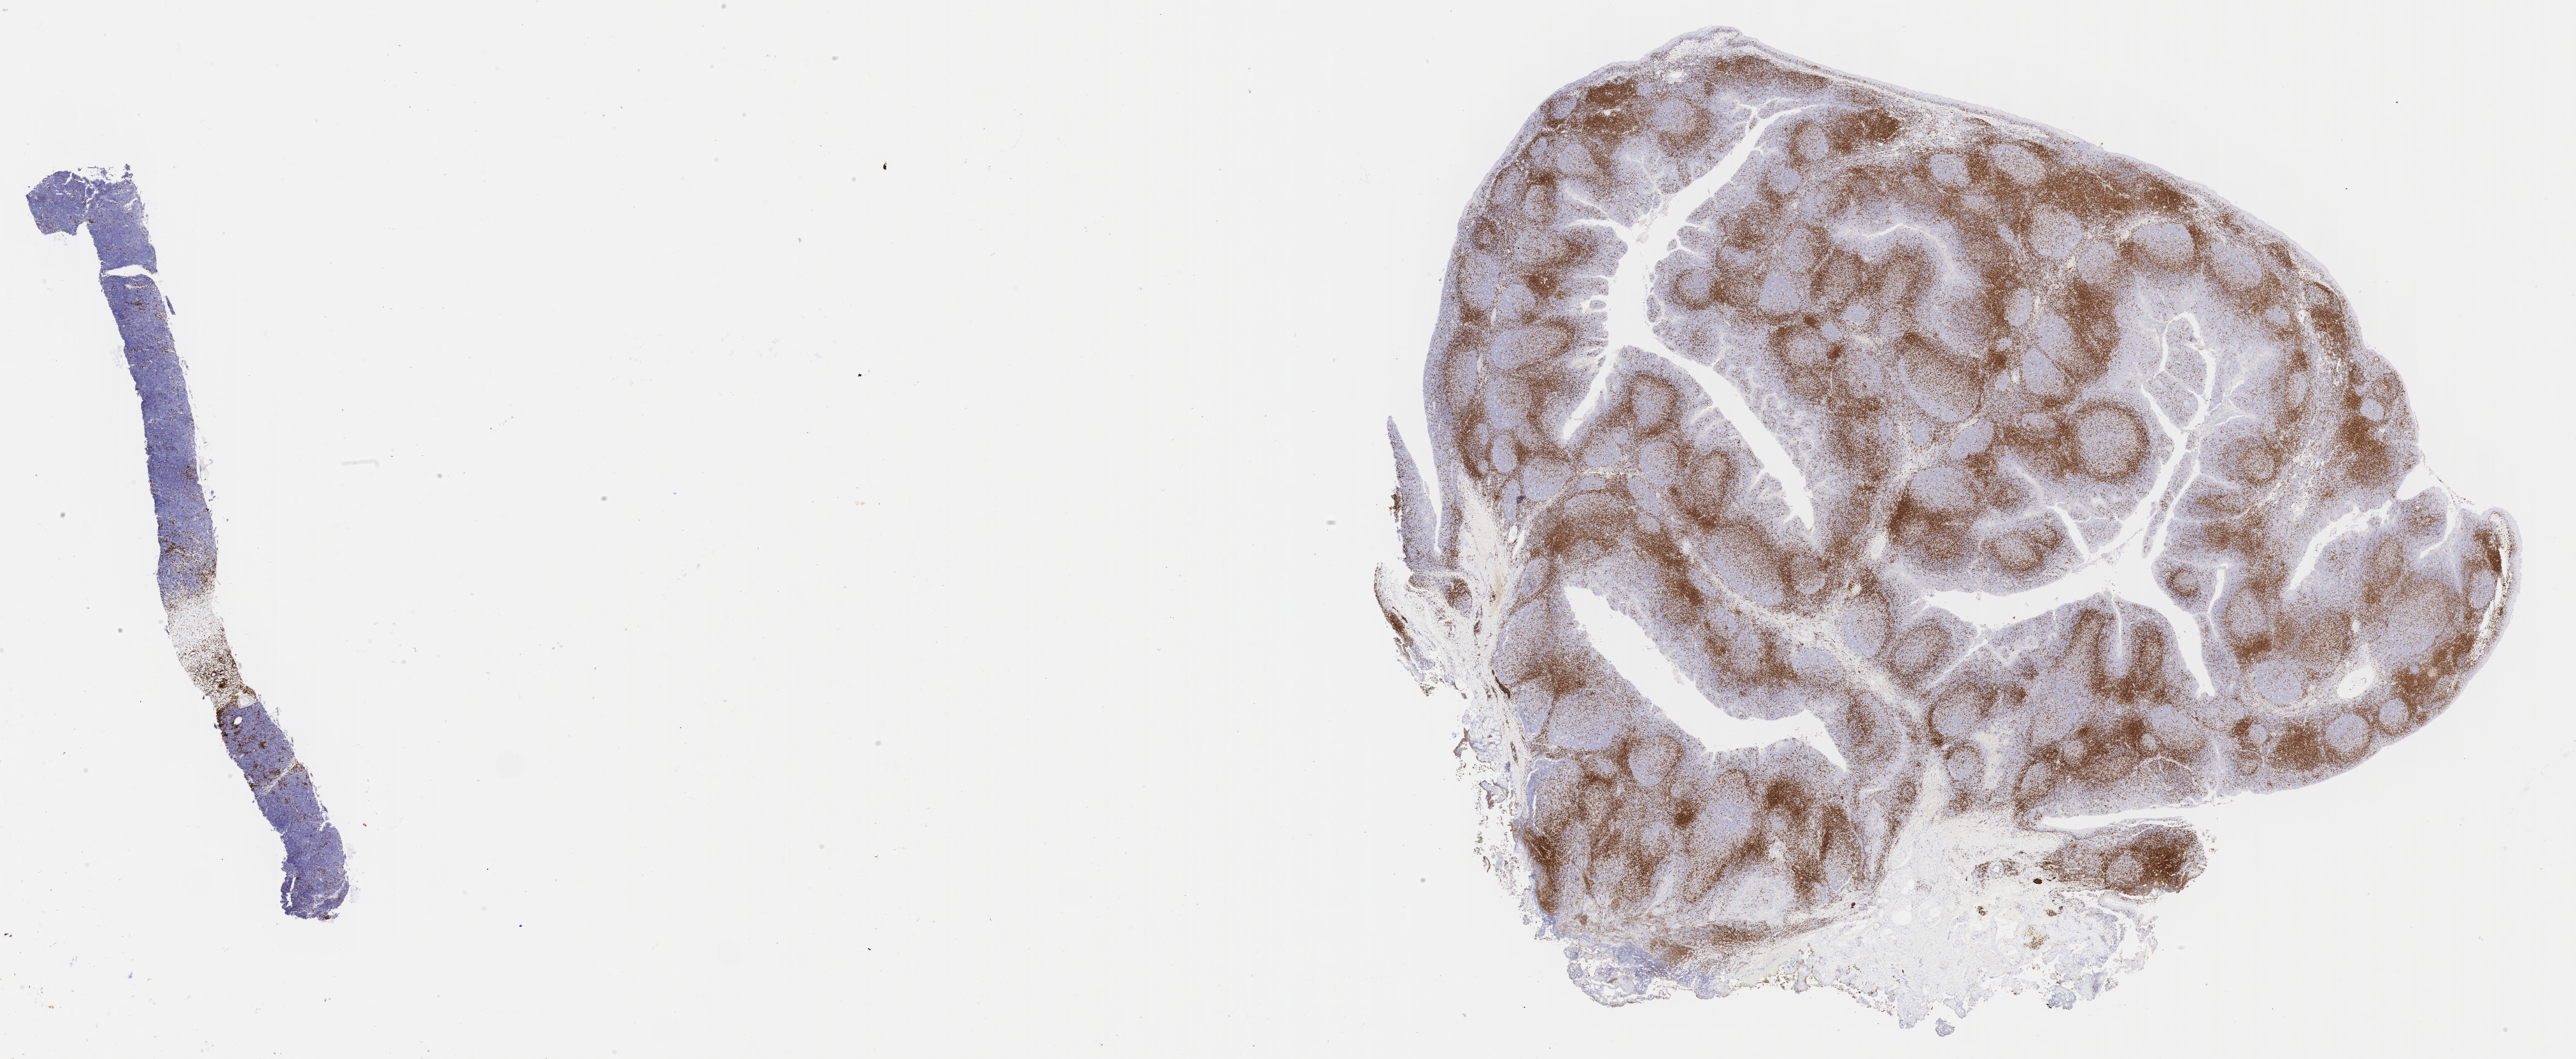
Immunohistochemistry (IHC) whole-slide image stained for CD3, low-resolution overview of the scanned area, about 32.7 x 13.4 mm, specimen: tumor tissue. Patient: male, age at initial diagnosis 7 years.
• diagnosis: Neoplasm, uncertain whether benign or malignant